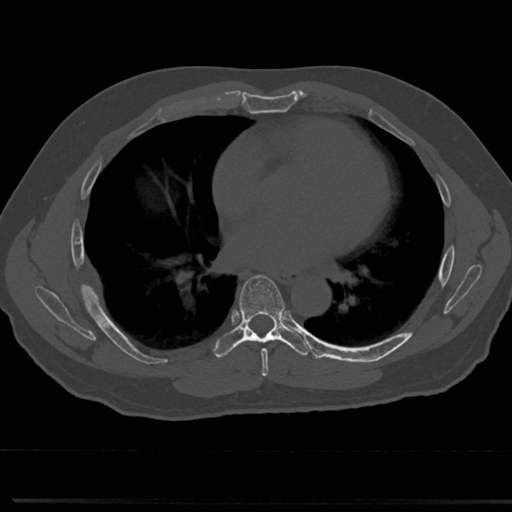
CT including the spine, one axial slice. Position 416 of 817 along the scan axis. Reconstruction kernel Br40s/3. 120 kVp. Bone window (W 1800 / L 400 HU). 0.5 mm slice thickness. 512 × 512 image matrix, field of view 355 × 355 mm. Patient: male, 61 years. From the clinical record (not read from this slice): primary cancer: prostate.
Annotated regions visible in this slice (semi-automatic segmentation, software-assisted and operator-edited):
- T6 vertebra: bounding box [x1, y1, x2, y2] px = [241, 281, 286, 362]
- T7 vertebra: [239, 275, 286, 335]